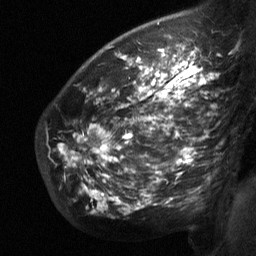
Breast MRI (dynamic contrast-enhanced), one sagittal slice. Dynamic contrast-enhanced study with each time point stored as its own series, time point 2 of 3 at this slice position (early post-contrast, ordered by acquisition time). 1.5 T. TE 4.8 ms, TR 27 ms. 2 mm slice thickness. 256 × 256 image matrix. Female patient, age 50 years. From the clinical record (not read from this slice): setting: breast cancer imaged before/during neoadjuvant chemotherapy; receptor status: HER2-positive.
Outlined on this slice (semi-automatic segmentation, software-assisted and operator-edited):
- analysis volume of interest (the breast-tissue region the enhancement analysis was run in; not a lesion): box from (x=59, y=62) to (x=214, y=213) px
- tumour enhancement mask (voxels above the 90 % enhancement threshold inside the analysis volume of interest): (x=70, y=62)–(x=213, y=202)